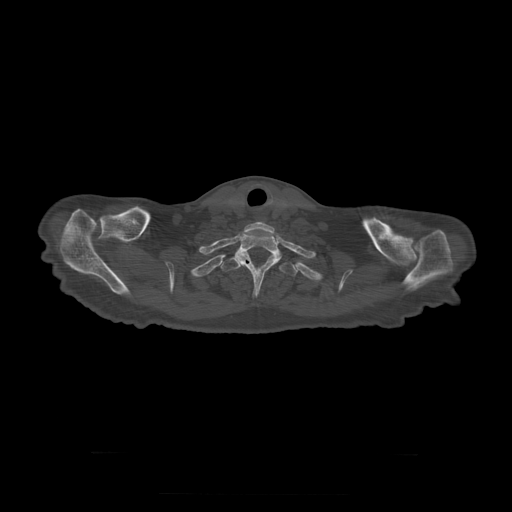
CT including the spine, one axial slice. Position 284 of 397 along the scan axis. Reconstruction kernel STANDARD. Bone window (W 1800 / L 400 HU). 512 × 512 image matrix, field of view 510 × 510 mm. Patient age 73 years. From the clinical record (not read from this slice): primary cancer: prostate.
Structures marked on this image (semi-automatically segmented with operator editing):
- T1 vertebra: bounding box (x1, y1, x2, y2) in pixels: (235, 231, 281, 293)
- T2 vertebra: (221, 257, 298, 277)